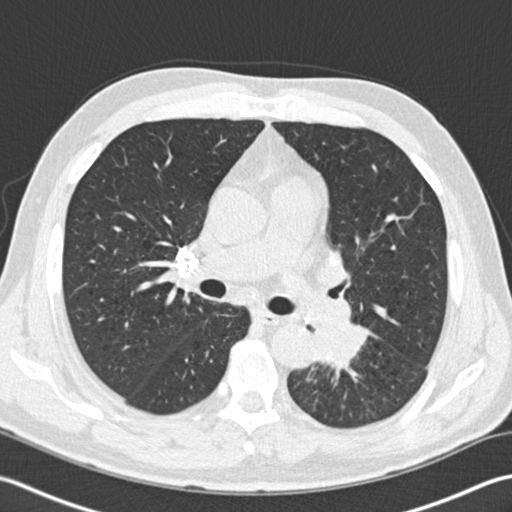
Low-dose screening chest CT, one axial slice. Slice 104 of 170 in the series (ordered by position). Lung window (W 1500 / L -600 HU). 2 mm slice thickness. 512 × 512 image matrix, field of view 350 × 350 mm.
Outlined on this slice (manually delineated by an expert):
- lesion 1 (tumor, lower lobe of left lung): box from (x=316, y=321) to (x=368, y=369) px